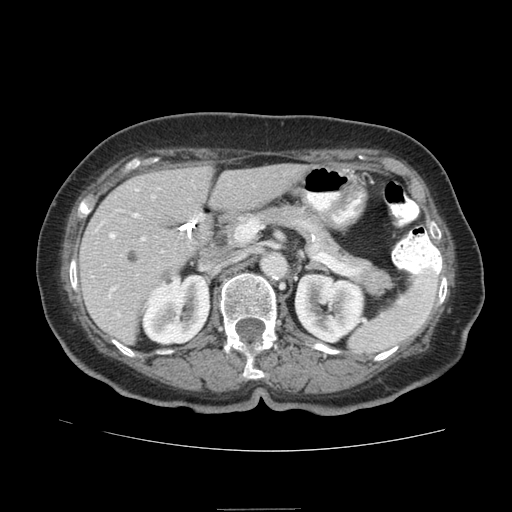
Contrast-enhanced abdominal CT (liver protocol), one axial slice. Position 40 of 95 along the scan axis. Reconstruction kernel STANDARD. 140 kVp. Soft-tissue window (W 400 / L 40 HU). 512 × 512 image matrix, field of view 360 × 360 mm. Case-level facts recorded for this patient, not image findings: diagnosis: hepatocellular carcinoma (patient treated with transarterial chemoembolisation; whether this scan precedes or follows treatment is not stated here); TNM stage (as recorded): Stage-IVA; Child-Pugh class: B; tumour differentiation: moderately differentiated; tumour nodularity: uninodular.
Structures marked on this image (semi-automatic segmentation, software-assisted and operator-edited):
- liver parenchyma outside the tumour (the mass and vessels are separate outlines, so this box may not span the whole liver): bounding box (x1, y1, x2, y2) in pixels: (78, 164, 308, 344)
- liver vessels: (96, 189, 202, 315)